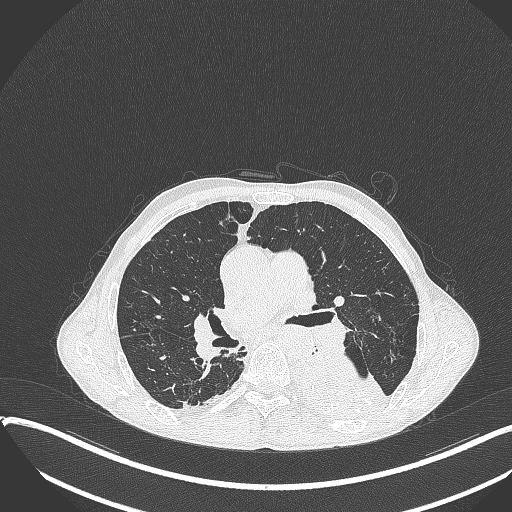
Chest CT, one axial slice. Reconstruction kernel B70f. 120 kVp. Lung window (W 1500 / L -600 HU). 1 mm slice thickness. 512 × 512 image matrix. Patient: male, 57 years. From the clinical record (not read from this slice): clinical TNM (as recorded): T4 N0 M0.
Structures marked on this image (bounding box drawn by a radiologist):
- lung tumour (recorded histology: squamous cell carcinoma): box from (x=287, y=351) to (x=394, y=425) px